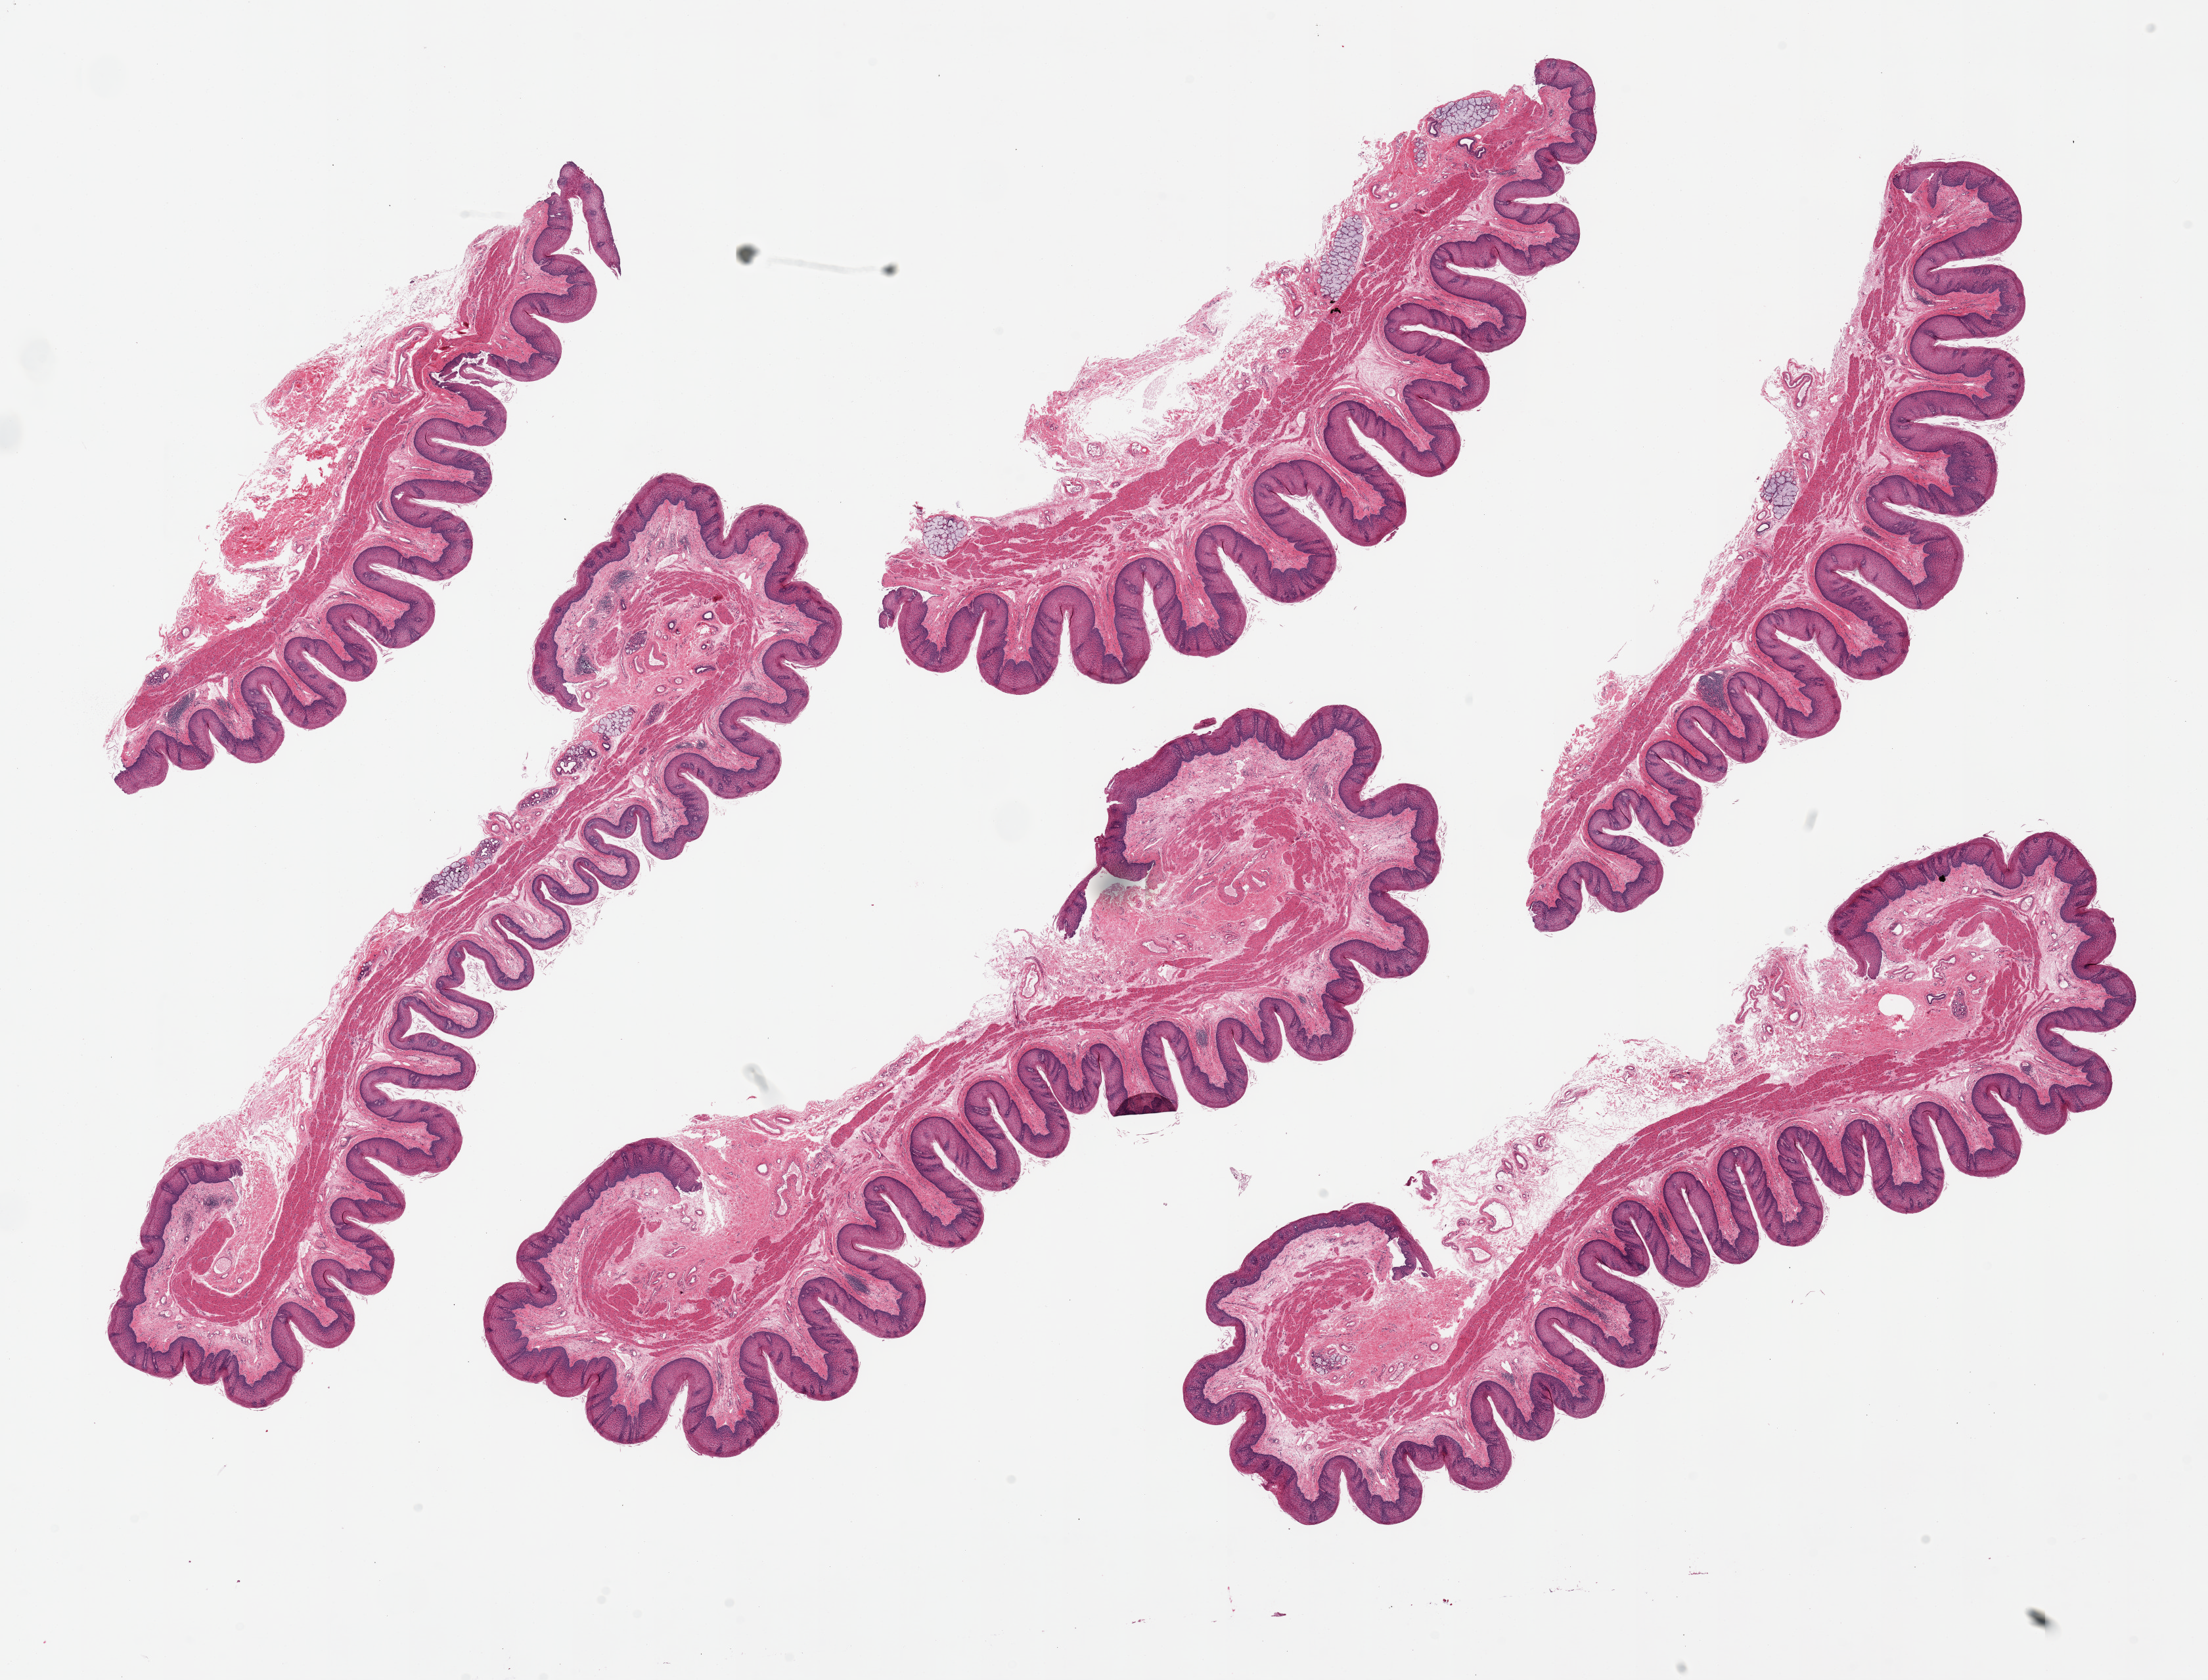
H&E whole-slide image, low-resolution overview of the scanned area, about 26.6 x 20.2 mm (acquisition: 20x scan), PAXgene-fixed paraffin-embedded (PFPE) section, sampled site (target tissue): esophageal mucous membrane, tissue donor sample.
Review note (as recorded): 6 pieces, up to 13x3mm; squamous mucosa well-preserved, ~25% thickness.